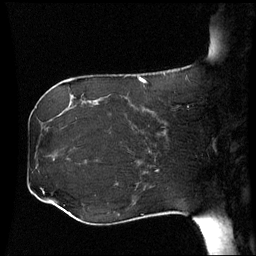
Breast MRI (dynamic contrast-enhanced), one sagittal slice. Position 21 of 60 along the scan axis. Dynamic contrast-enhanced series, image 2 of 3 at this slice position (ordered by acquisition). 1.5 T. TE 4.2 ms, TR 8.9 ms. 2.5 mm slice thickness. 256 × 256 image matrix, field of view 230 × 230 mm. Female patient, age 42 years. From the clinical record (not read from this slice): setting: breast cancer imaged before/during neoadjuvant chemotherapy; receptor status: HER2-positive.
Outlined on this slice (semi-automatically segmented with operator editing):
- analysis volume of interest (the breast-tissue region the enhancement analysis was run in; not a lesion): box from (x=106, y=102) to (x=173, y=150) px
- tumour enhancement mask (voxels above the 70 % enhancement threshold inside the analysis volume of interest): (x=131, y=104)–(x=143, y=112)